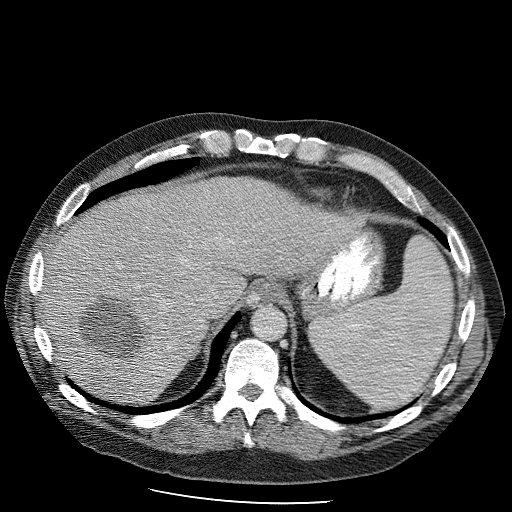
Contrast-enhanced abdominal CT (liver protocol), one axial slice. Position 81 of 98 along the scan axis. 120 kVp. Soft-tissue window (W 400 / L 40 HU). 2.5 mm slice thickness. 512 × 512 image matrix. From the clinical record (not read from this slice): diagnosis: hepatocellular carcinoma (patient treated with transarterial chemoembolisation; whether this scan precedes or follows treatment is not stated here); TNM stage (as recorded): Stage-II; Child-Pugh class: B; tumour nodularity: uninodular.
Outlined on this slice (semi-automatic segmentation, software-assisted and operator-edited):
- liver parenchyma outside the tumour (the mass and vessels are separate outlines, so this box may not span the whole liver): bounding box [x1, y1, x2, y2] px = [37, 178, 360, 400]
- mass: [75, 292, 155, 364]
- liver vessels: [197, 297, 206, 314]